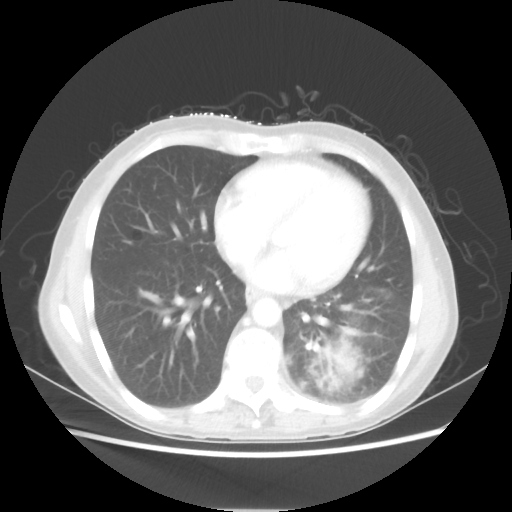
Chest CT, one axial slice. Lung window (W 1500 / L -600 HU). 5 mm slice thickness. 512 × 512 image matrix. Patient: female, 53 years. From the clinical record (not read from this slice): clinical TNM (as recorded): T3 N0 M0.
Annotated regions visible in this slice (bounding box drawn by a radiologist):
- lung tumour (recorded histology: adenocarcinoma): bounding box [x1, y1, x2, y2] px = [319, 328, 363, 391]